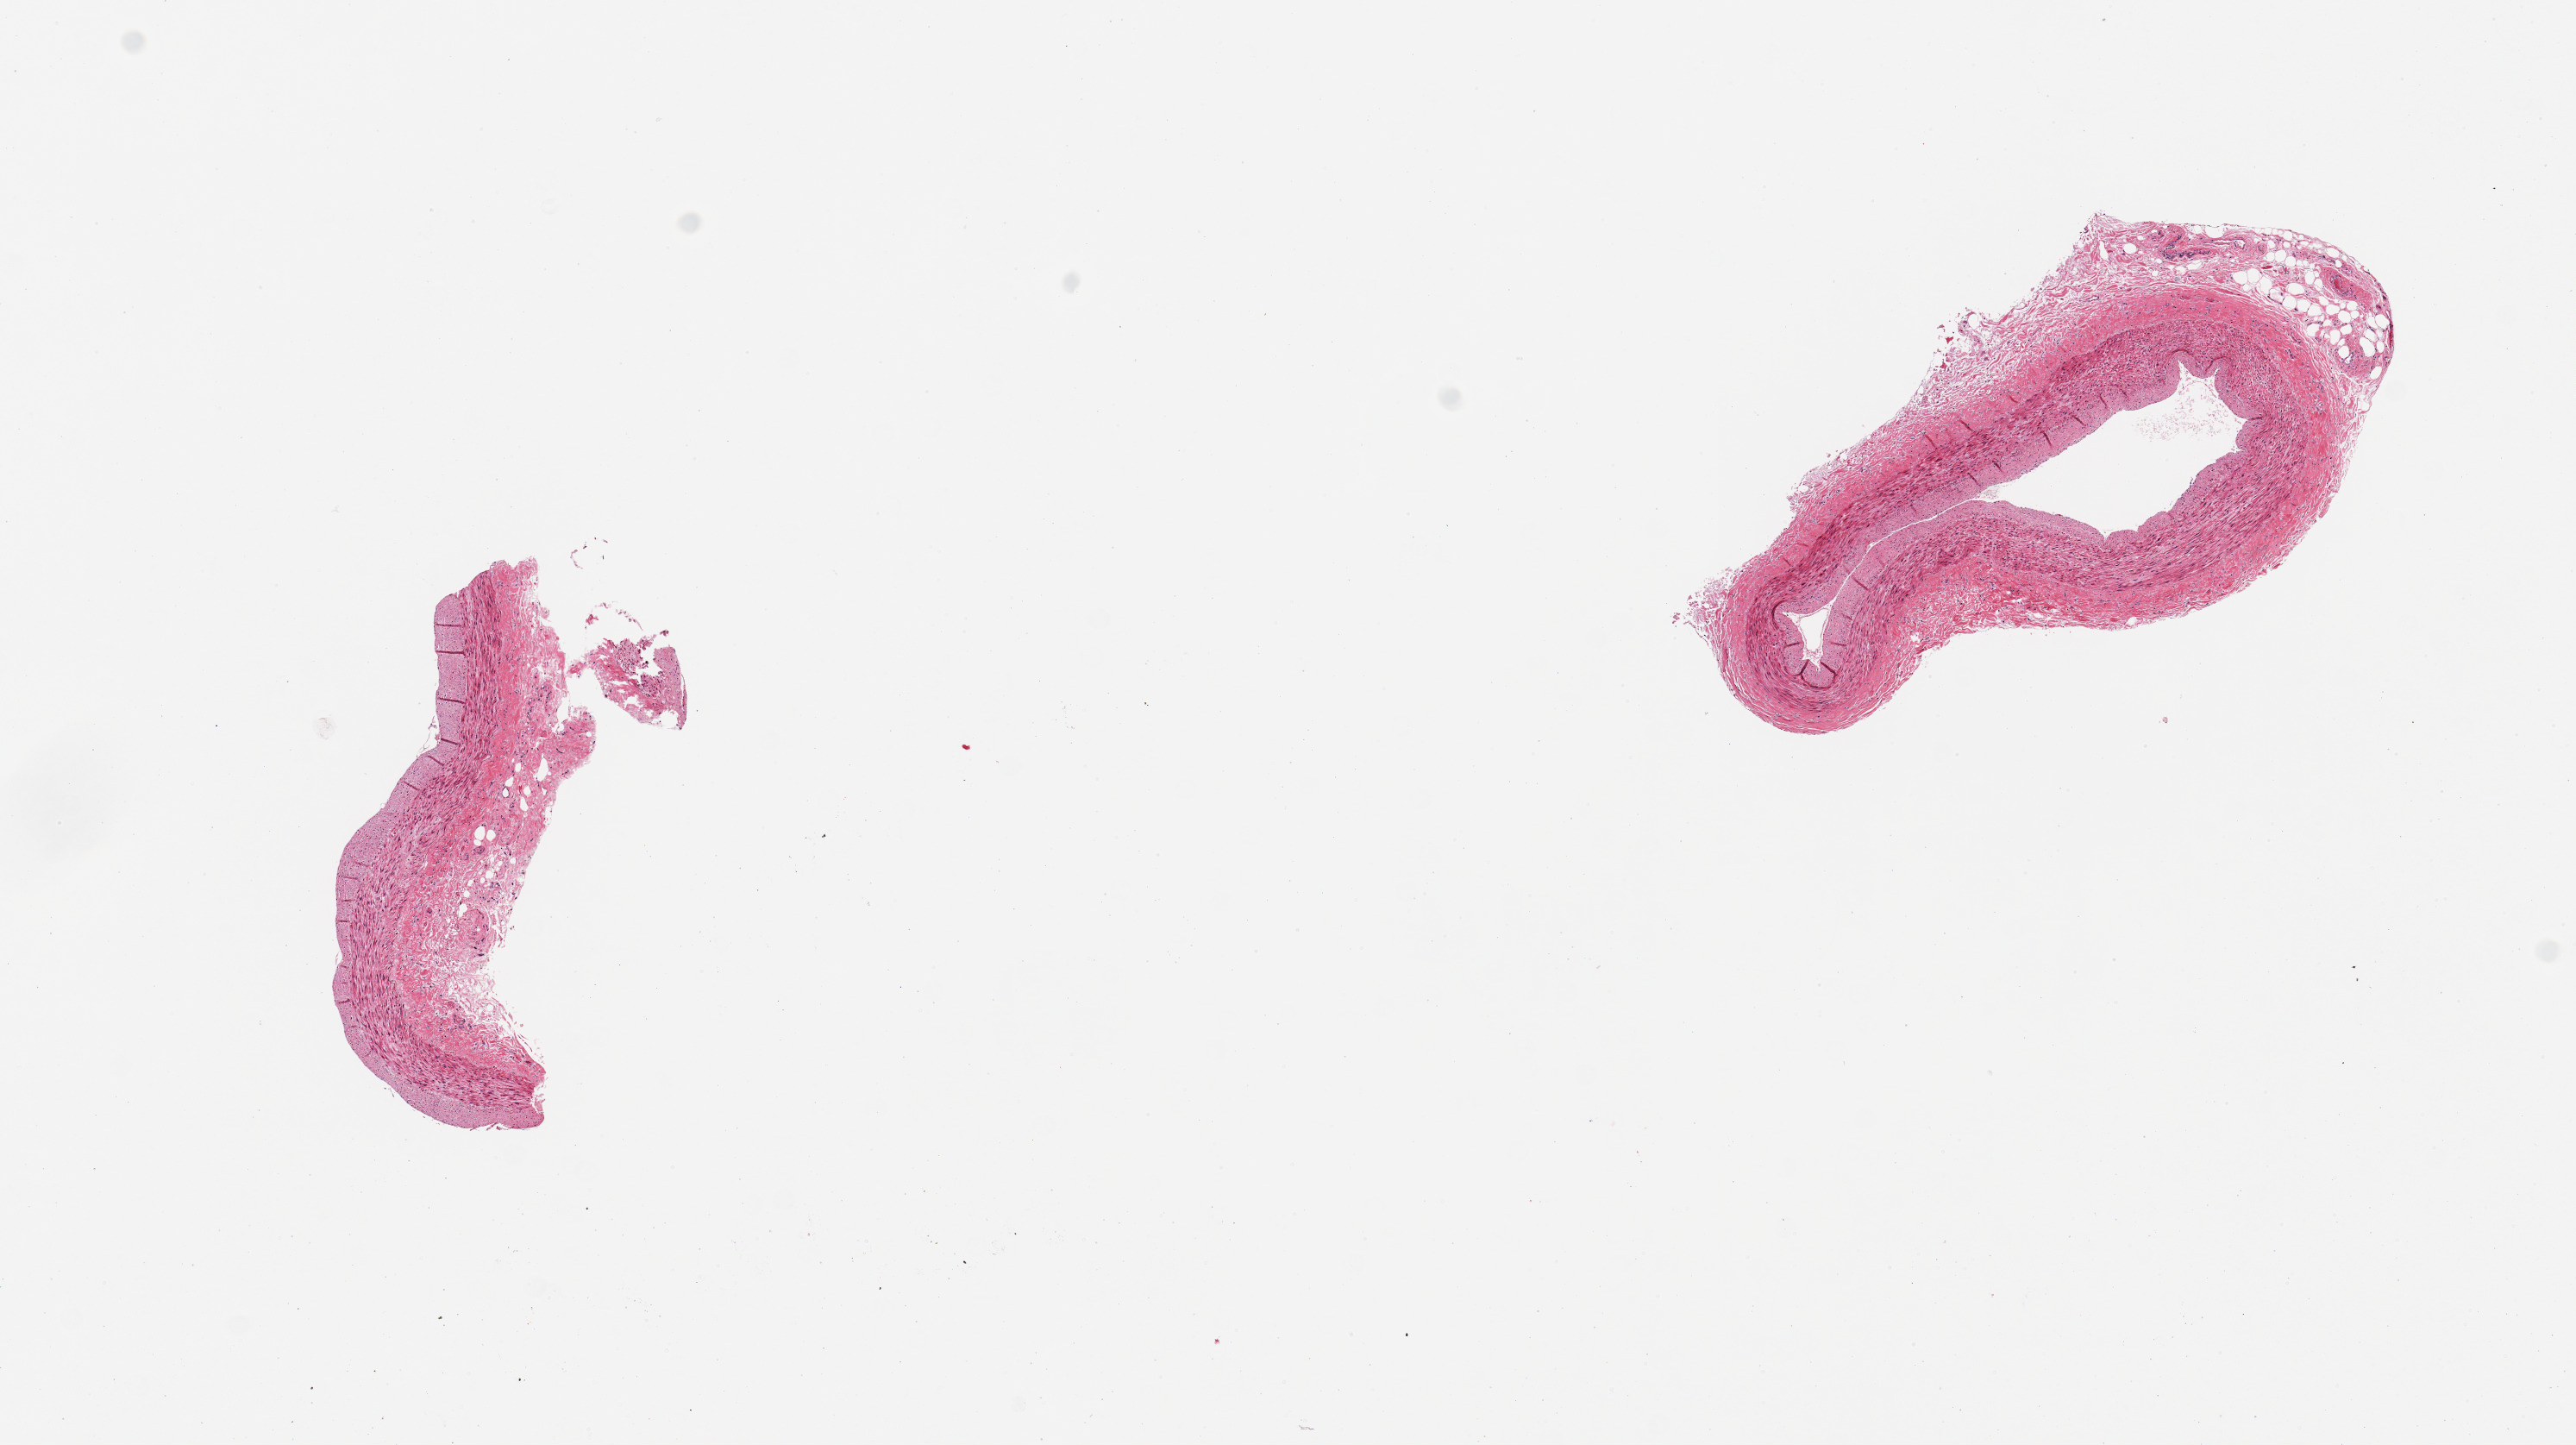
Digitized haematoxylin and eosin-stained section, whole scanned area (about 11.8 x 6.6 mm) shown as a low-resolution overview, PAXgene-fixed, paraffin-embedded tissue, section of coronary artery (target tissue), donor tissue sample. Donor: female.
Reviewer comment on this tissue sample: 2 pieces; no plaques; 10% external fat.